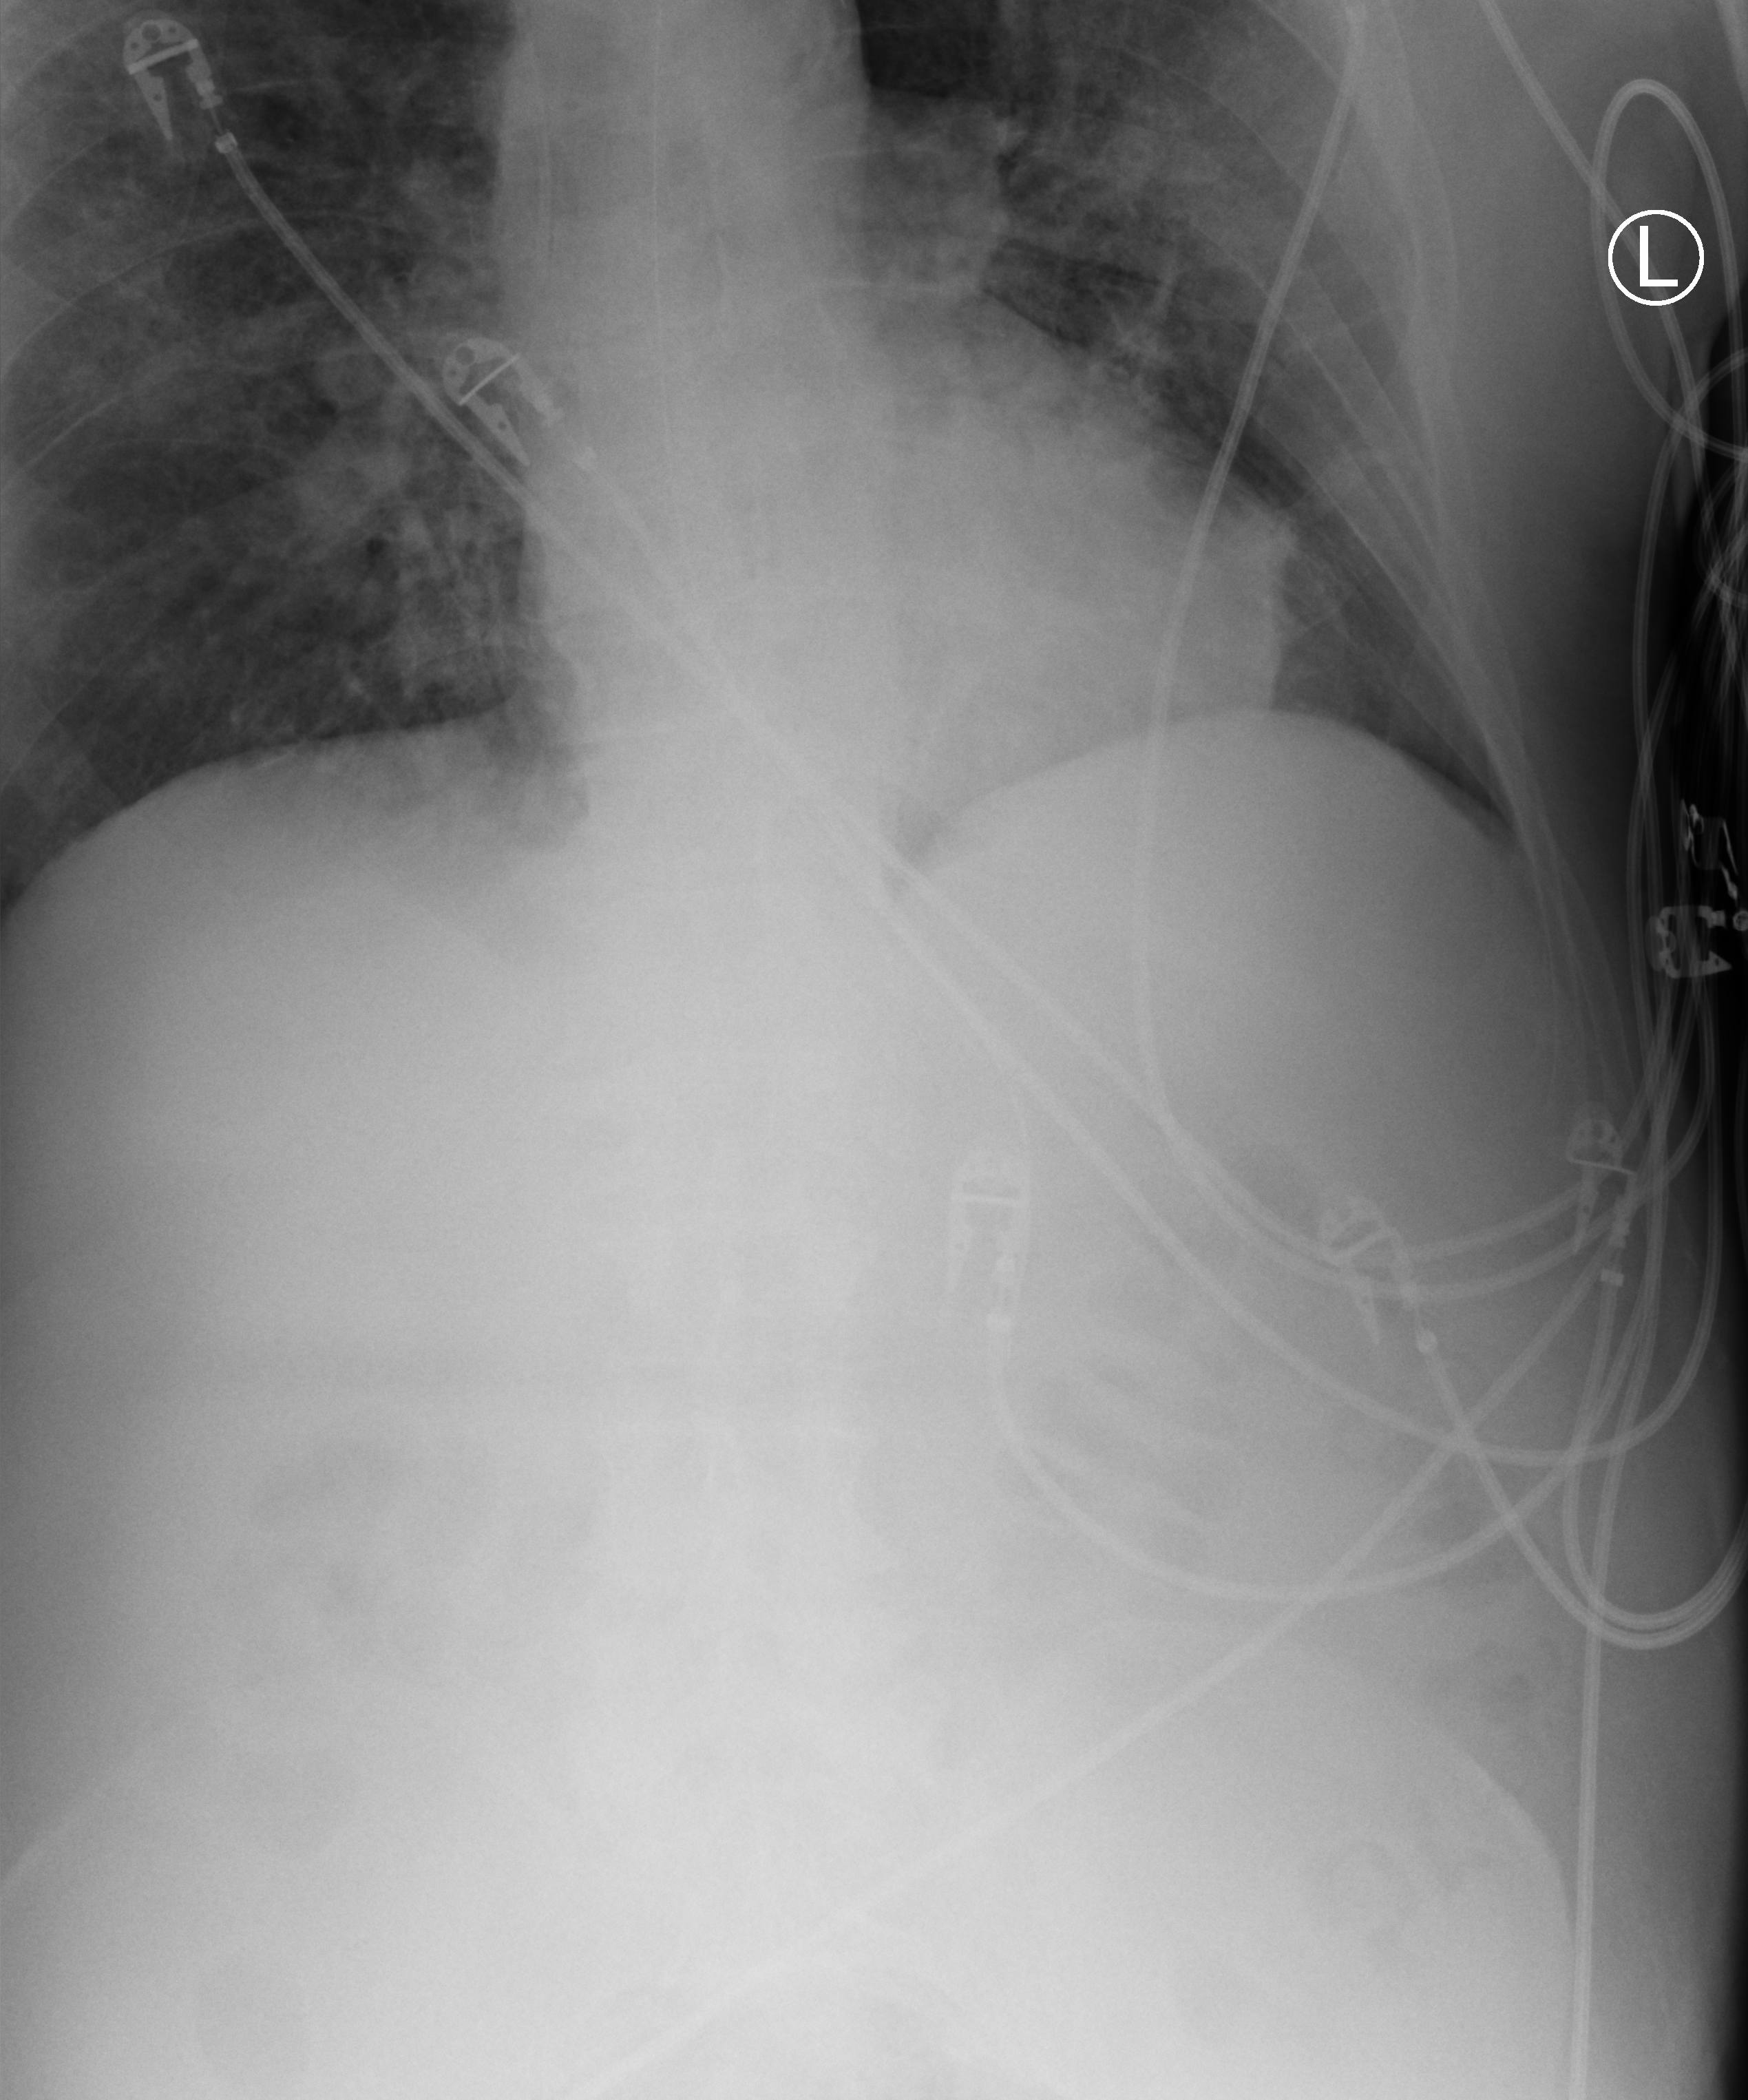
Bedside chest radiograph (computed radiography). Male patient hospitalised with COVID-19, age 75–90 years.
Admission-level facts for this patient (not findings on this image; timing relative to this image not recorded):
- admitted to intensive care during this hospital stay: yes
- diabetes (admission record): no
- smoking status (admission record): former